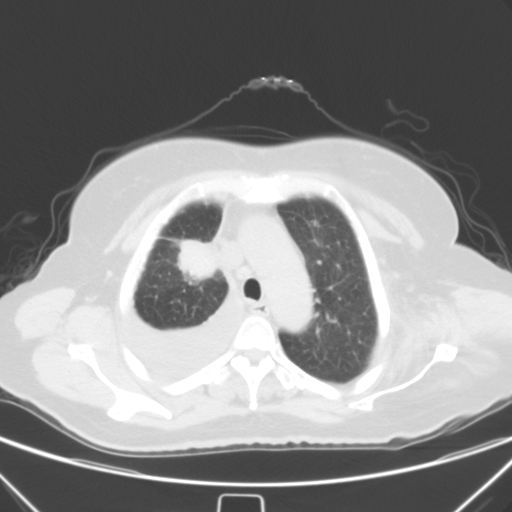
Chest CT, one axial slice; 120 kVp; lung window (W 1500 / L -600 HU); 512 × 512 image matrix, field of view 352 × 352 mm. Patient: female, 66 years. Case-level facts recorded for this patient, not image findings: clinical TNM (as recorded): T2 N0 M1.
Outlined on this slice (rectangle marked by the reading radiologist):
- lung tumour (recorded histology: adenocarcinoma): bounding box <176,236,221,281> (left, top, right, bottom; pixels)